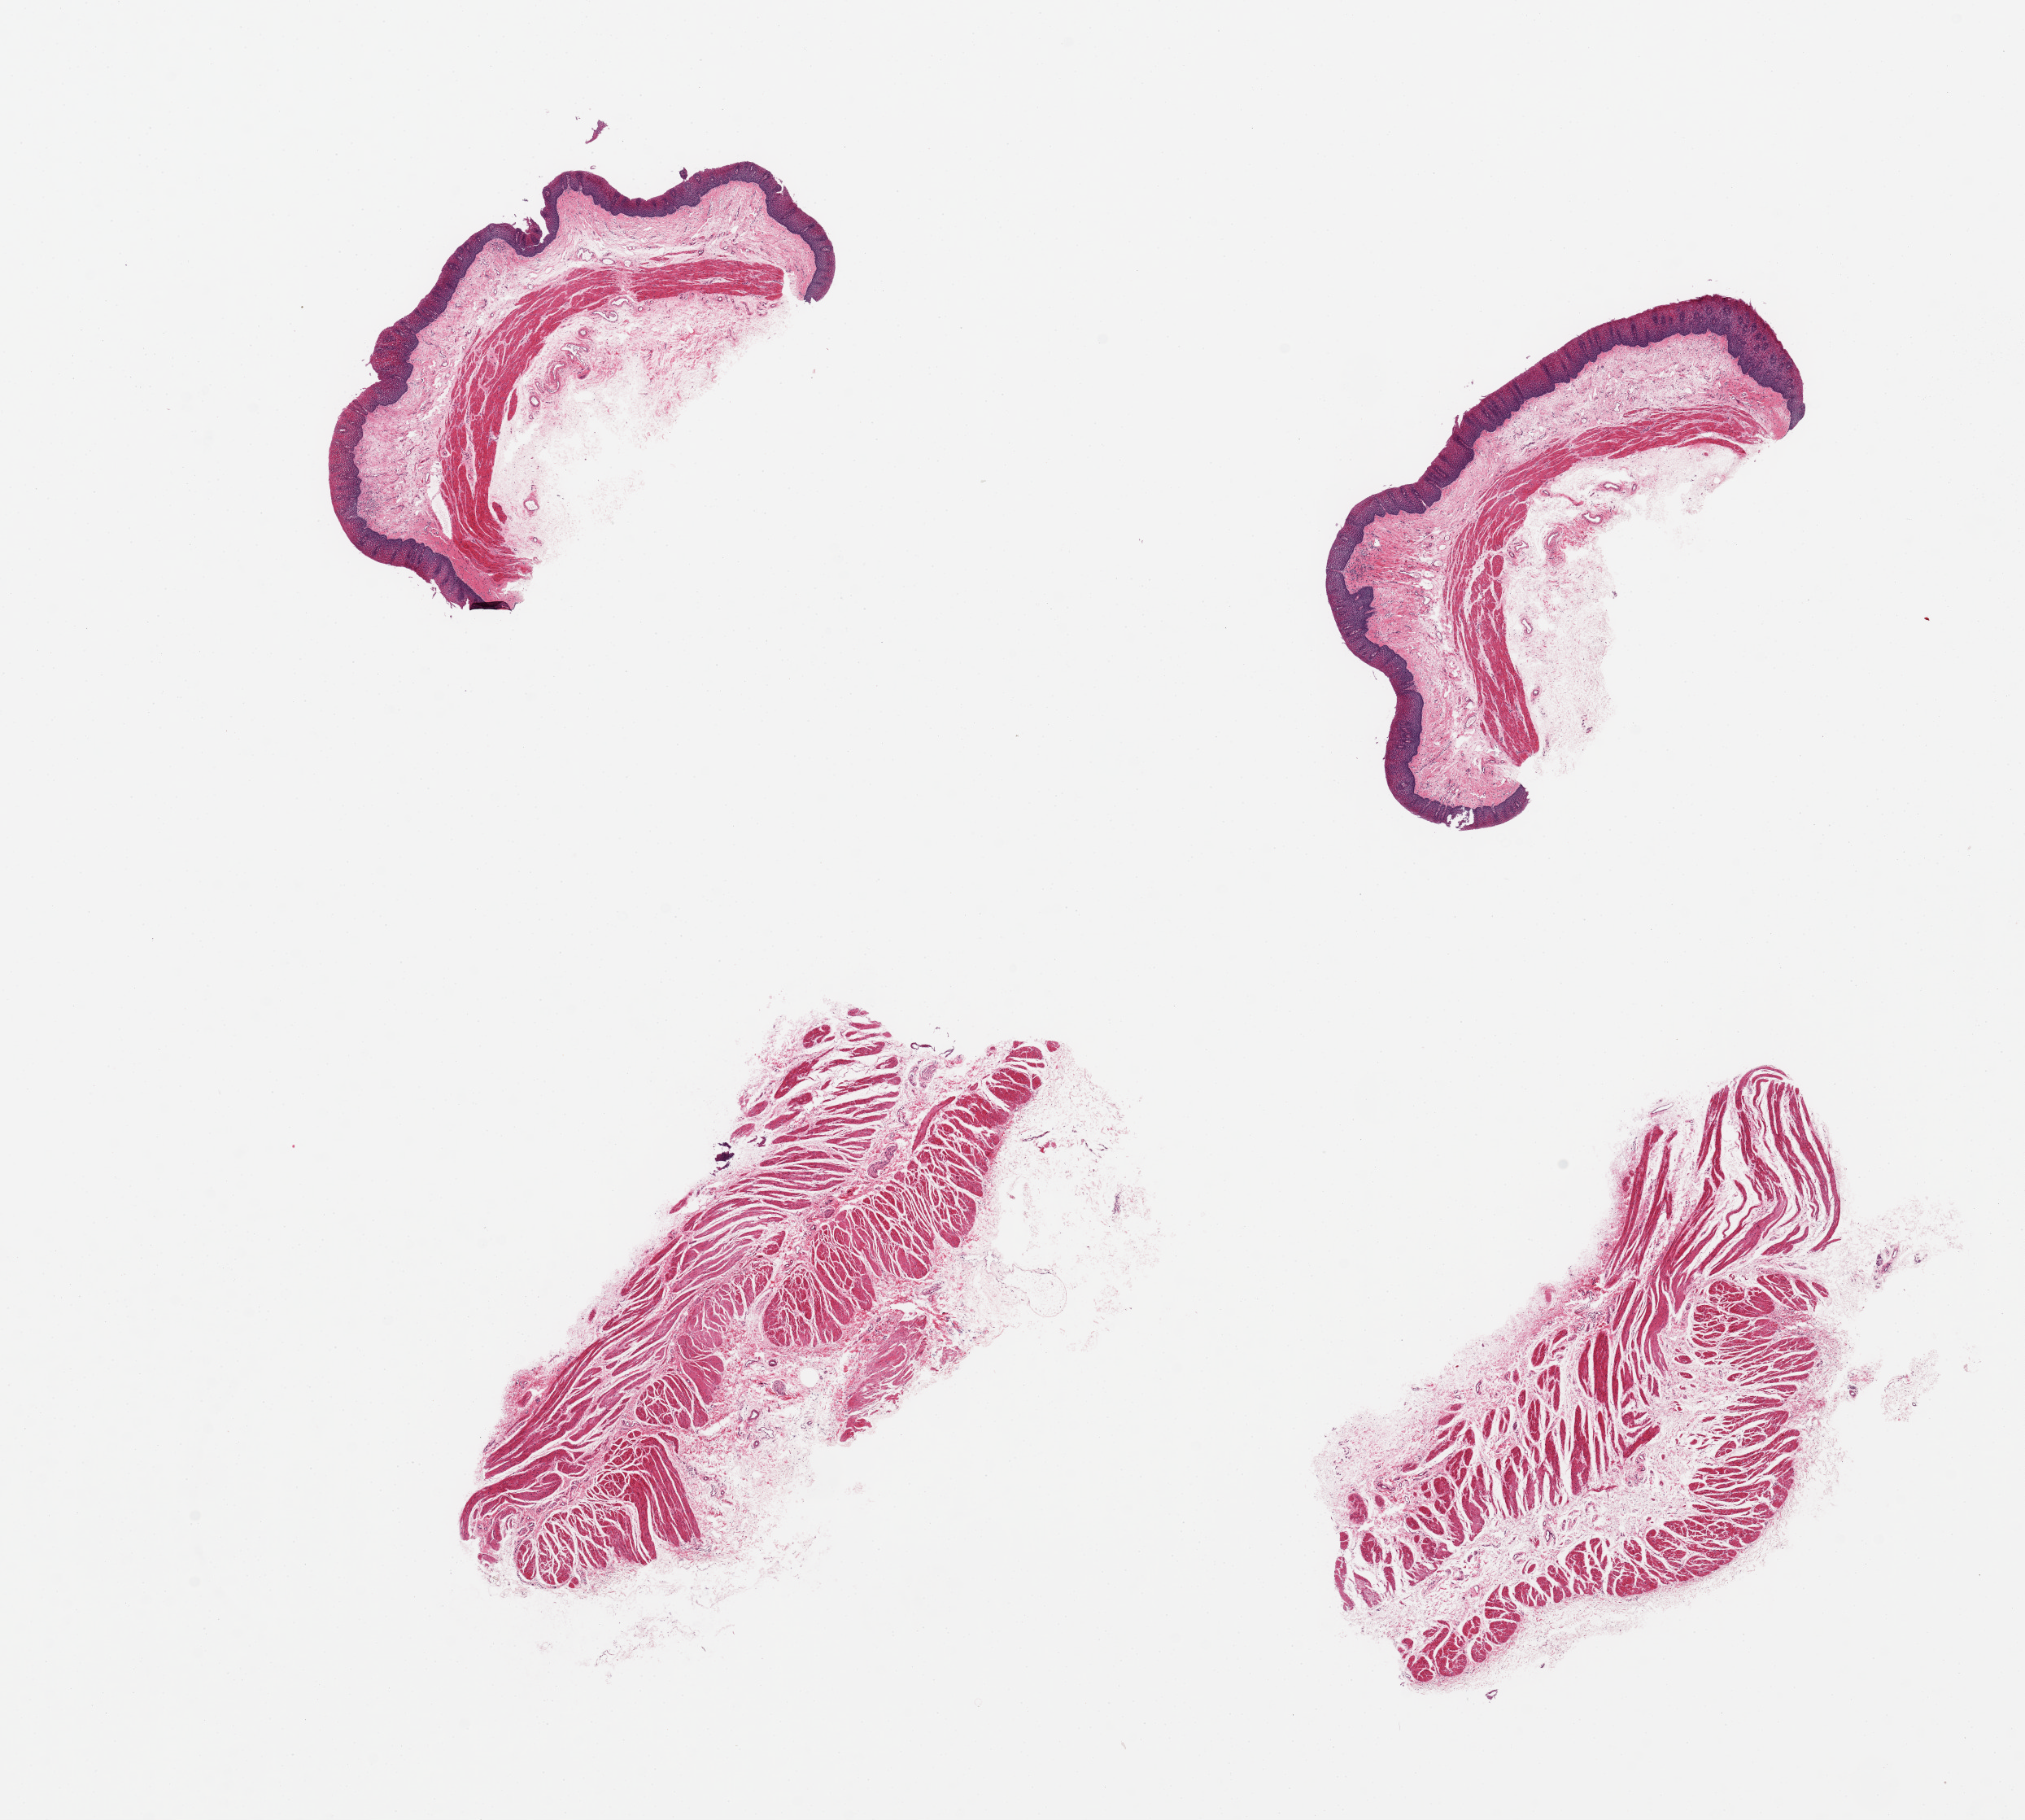
Haematoxylin and eosin whole-slide image — whole scanned area (about 19.7 x 17.7 mm, from a 20x scan) shown as a low-resolution overview. PAXgene-fixed, paraffin-embedded tissue. Section of gastroesophageal junction (target tissue). Tissue donor sample. Donor sex: female.
* review note (as recorded): 4 pieces, 2 are muscularis, two are esophageal mucosa and submucosa